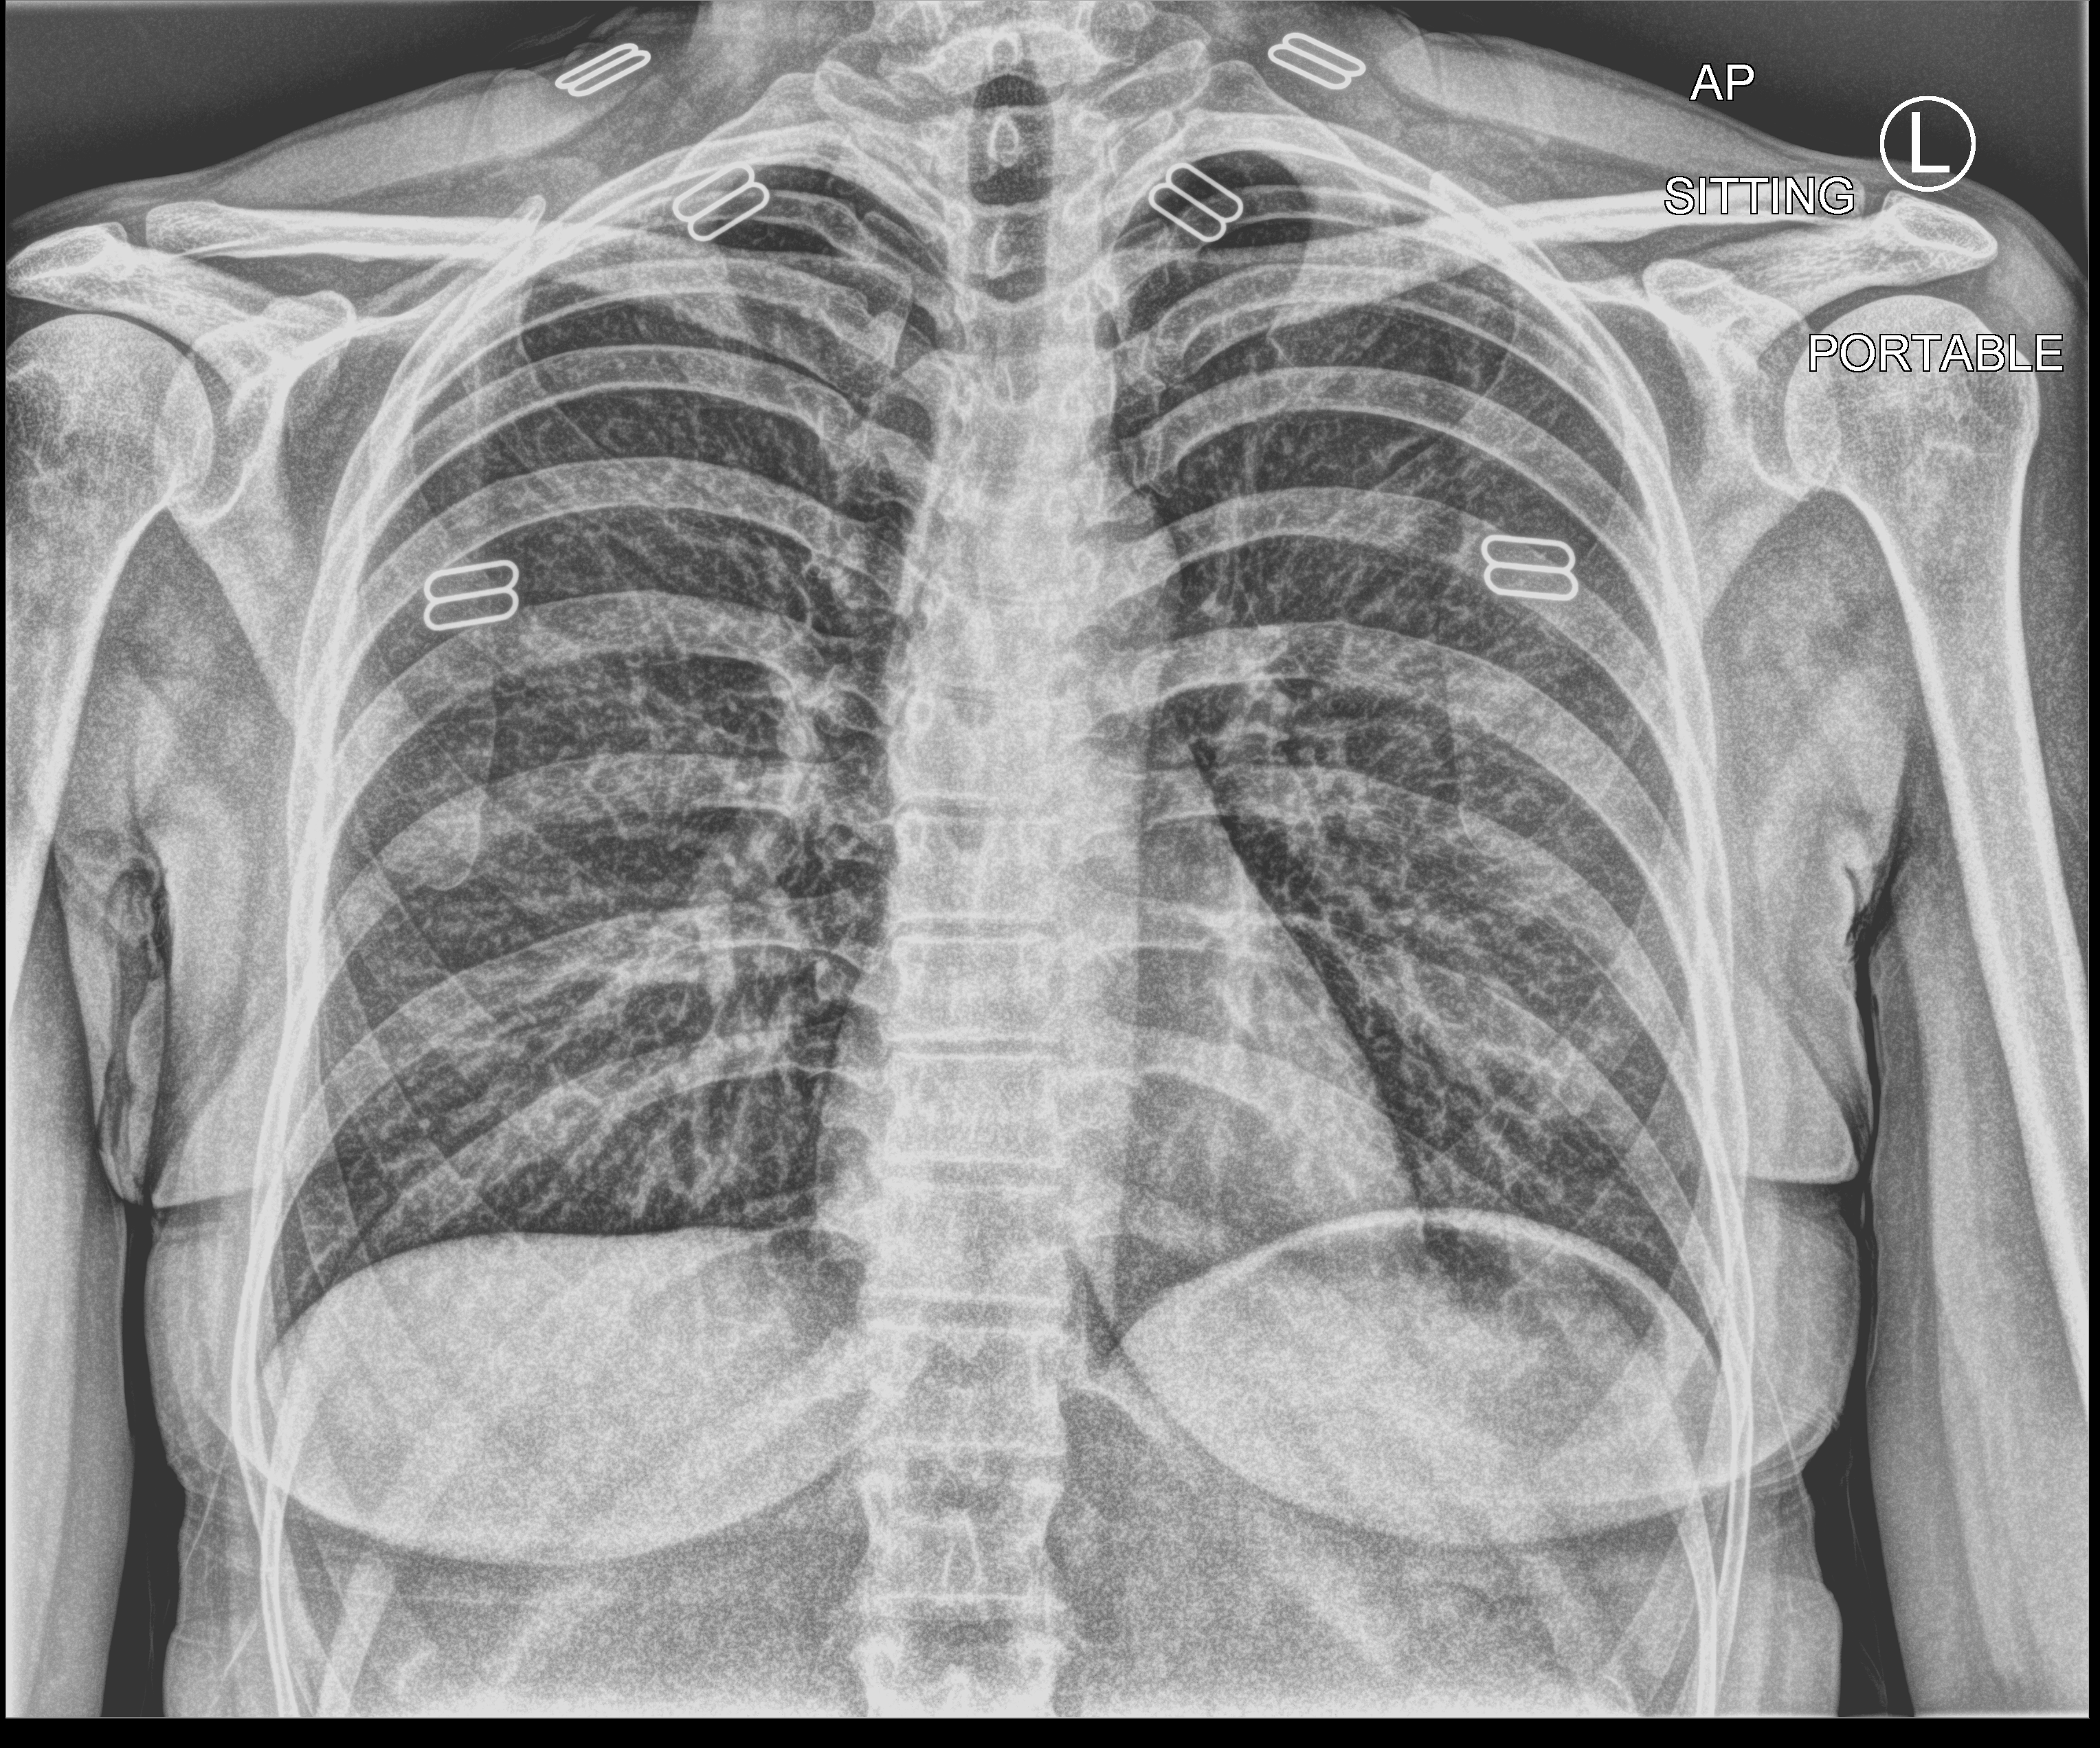
Bedside chest radiograph (computed radiography). Female patient hospitalised with COVID-19, age 18–59 years.
Admission-level facts for this patient (not findings on this image; timing relative to this image not recorded):
- admitted to intensive care during this hospital stay: no
- mechanically ventilated during this hospital stay: no